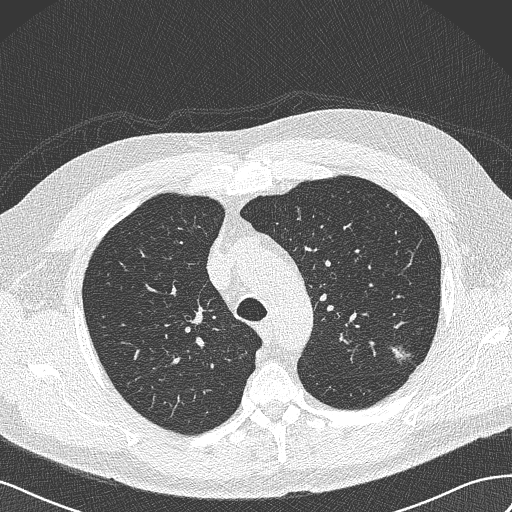
Low-dose screening chest CT, axial slice; first (baseline) screen; lung window (W 1500 / L -600 HU); 1 mm slice thickness; lung (sharp) reconstruction kernel (B50f); slice 111 of 462 in the series. Male, age 65 years at enrolment. Former smoker at enrolment.
Lesion marked by an expert reader, box from (x=383, y=340) to (x=419, y=371) px. The screening reader recorded 3 non-calcified nodules or masses ≥4 mm on this exam (left upper lobe, left upper lobe, right upper lobe); which of them this box marks is not recorded. Official screen result: positive, change unspecified: nodule(s) >= 4 mm or enlarging nodule(s), mass(es), or other non-specific abnormalities suspicious for lung cancer.